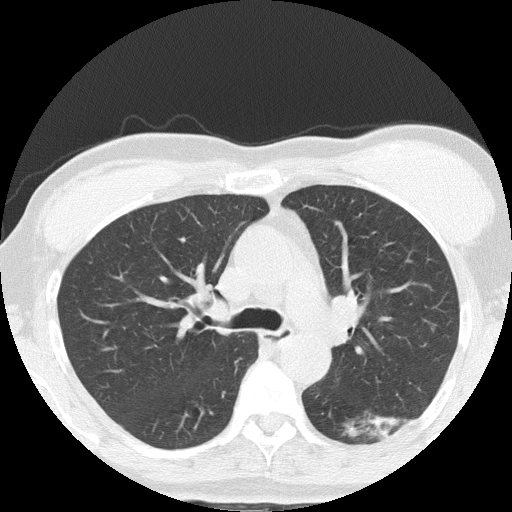
Chest CT (low-dose screening protocol), one axial image; third annual screen; lung window (W 1500 / L -600 HU); lung (sharp) reconstruction kernel (FC51). Female participant, aged 64 years at enrolment.
Expert reader's lesion annotation, box from (x=342, y=390) to (x=428, y=457) px. The screening reader recorded 3 non-calcified nodules or masses ≥4 mm on this exam; which of them this box marks is not recorded. Official screen result: positive, other.